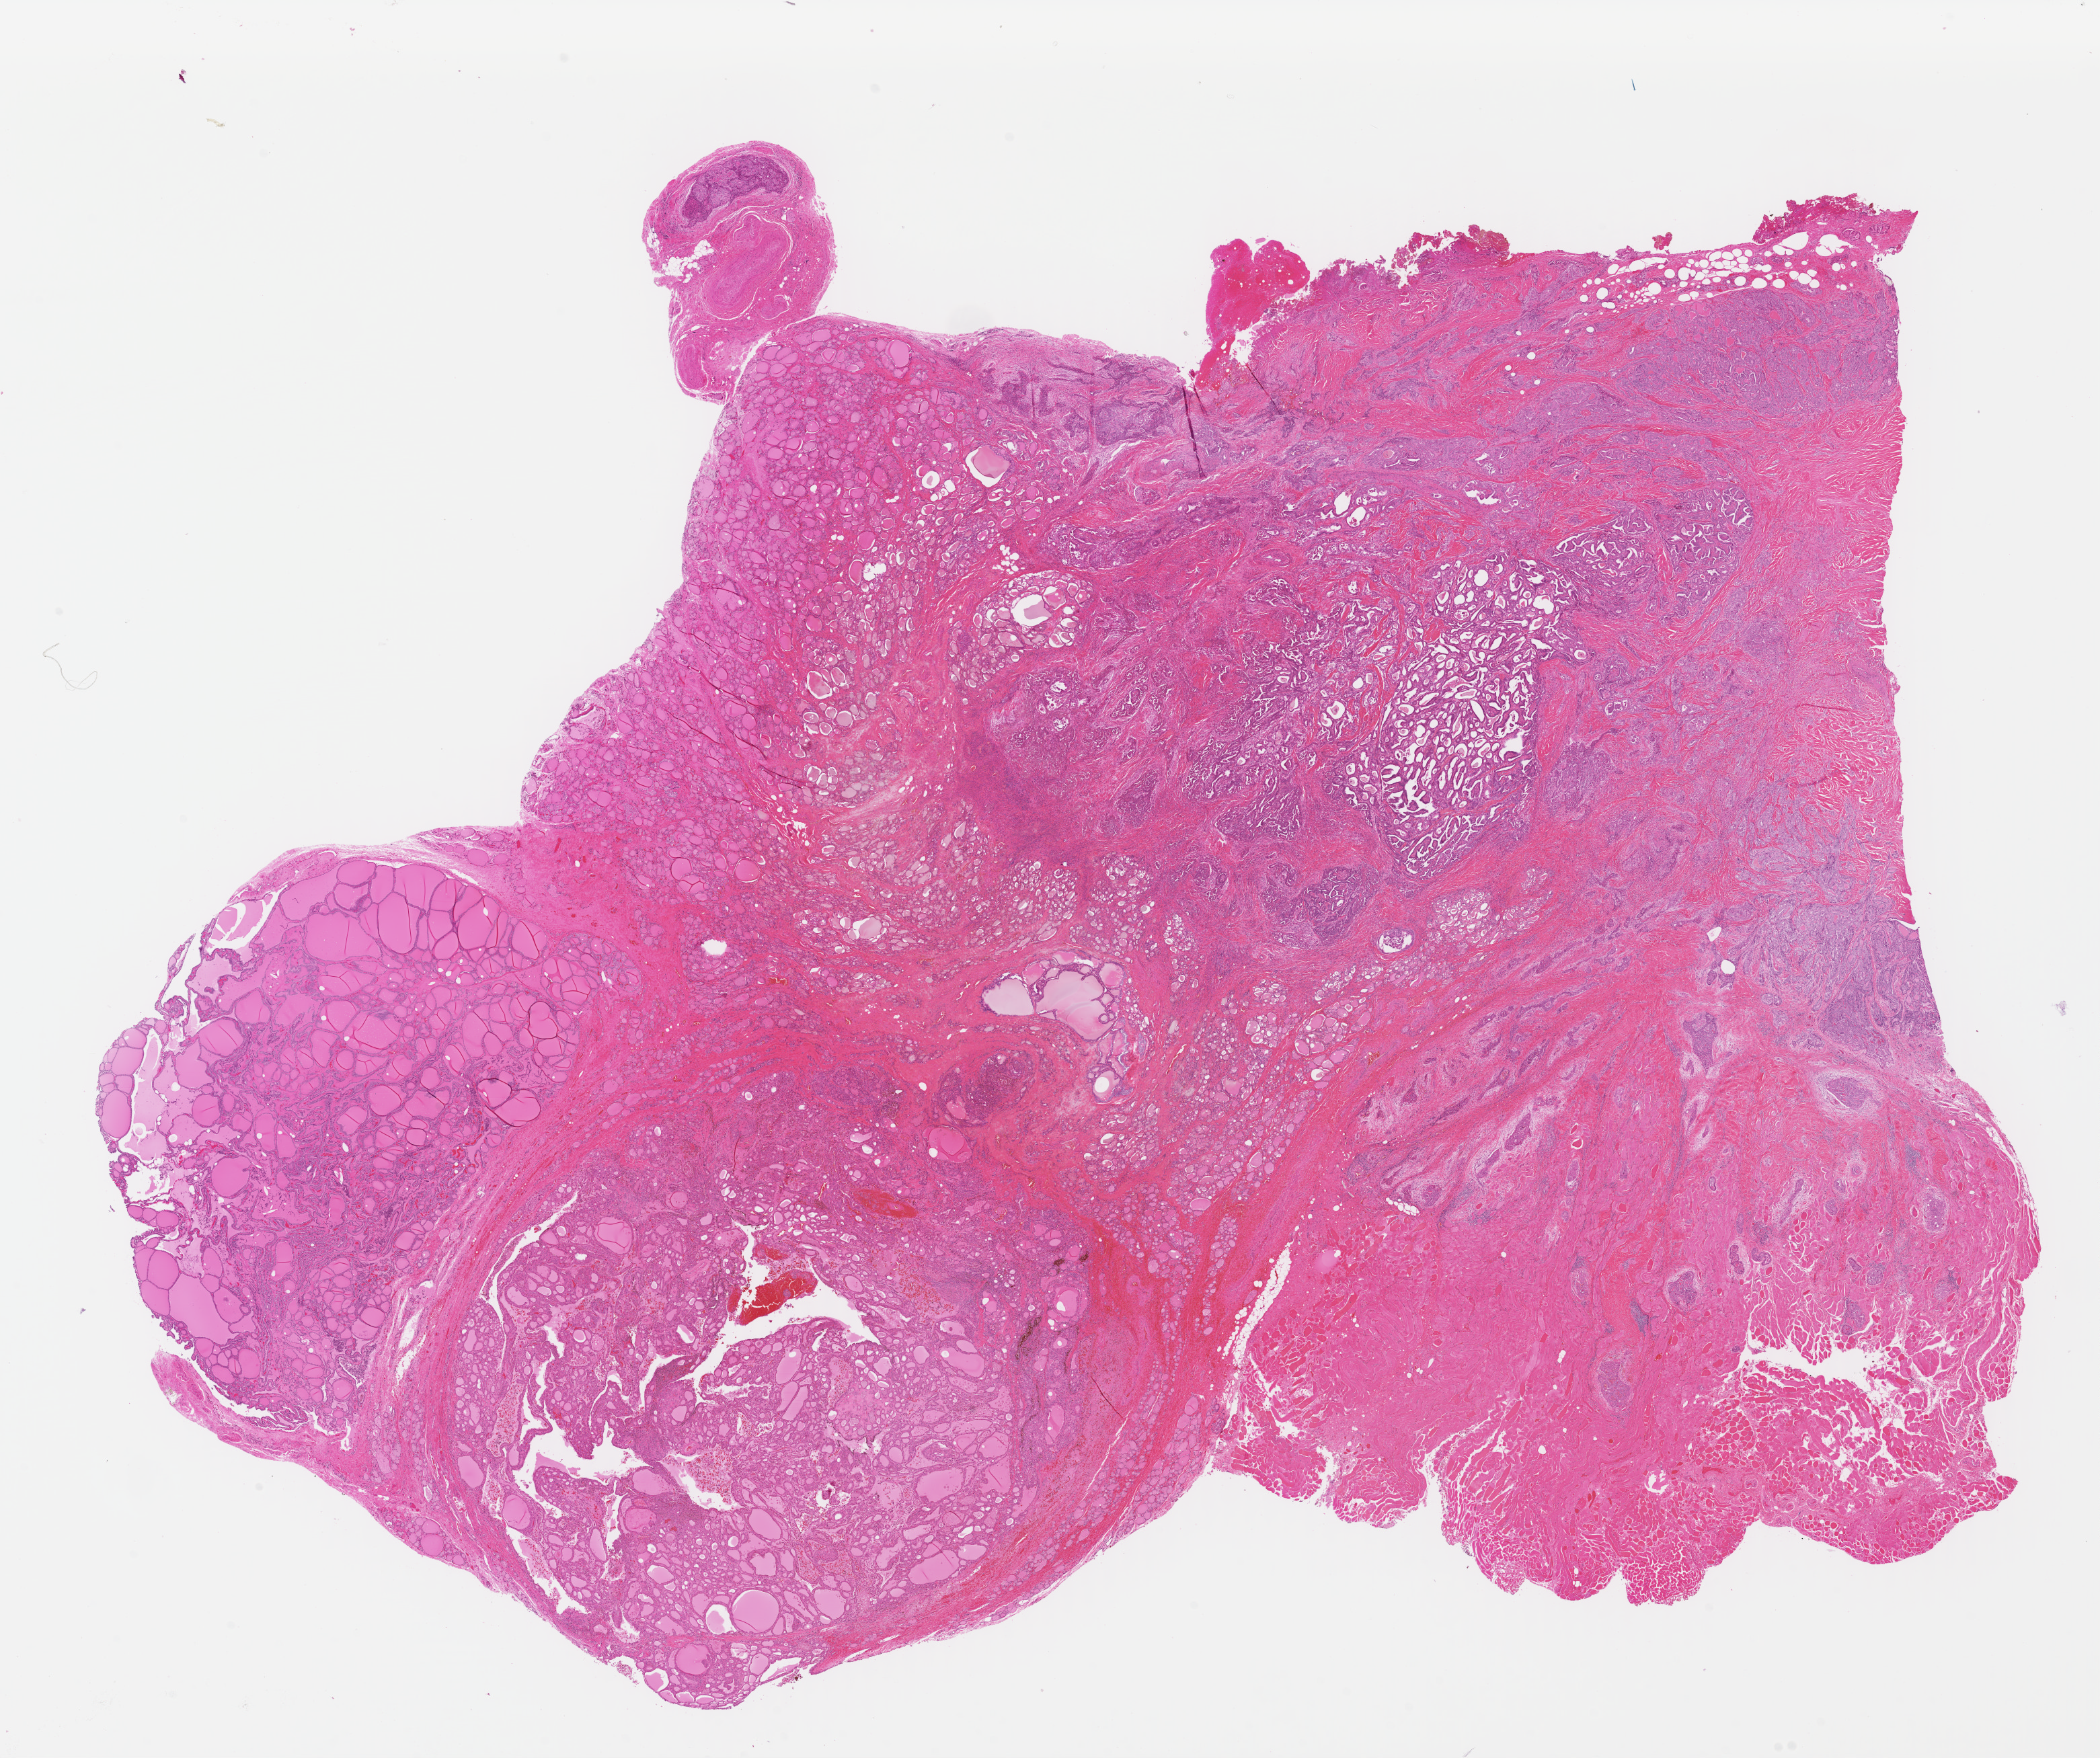
Digitized H&E tissue section (whole slide), a low-resolution overview of the entire scanned area, about 24.6 x 20.6 mm (slide scanned at 40x), formalin-fixed paraffin-embedded (FFPE) diagnostic section, thyroid, primary tumour sample. Male patient; age at initial diagnosis 81 years.
Laterality: left. Pathologic diagnosis: Papillary adenocarcinoma, NOS (thyroid gland). AJCC pathologic stage: IVC (6th edition).